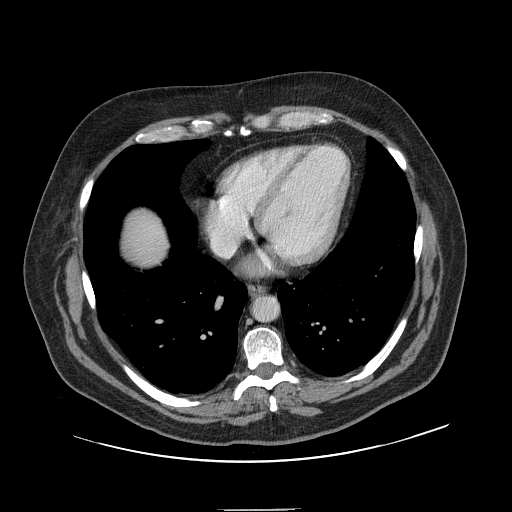
Contrast-enhanced abdominal CT, one axial slice. Slice 145 of 154 in the series (ordered by position). Intravenous contrast given. Soft-tissue window (W 400 / L 40 HU). 2.5 mm slice thickness. 512 × 512 image matrix. Male patient, age 61 years. From the clinical record (not read from this slice): diagnosis: colorectal cancer liver metastases, imaged before liver resection; multiple liver metastases: yes; largest metastasis: 2.6 cm.
Annotated regions visible in this slice (manually delineated by an expert):
- liver: bounding box [x1, y1, x2, y2] px = [126, 212, 166, 264]
- planned liver remnant (the part of the liver to remain after resection): [127, 212, 166, 266]